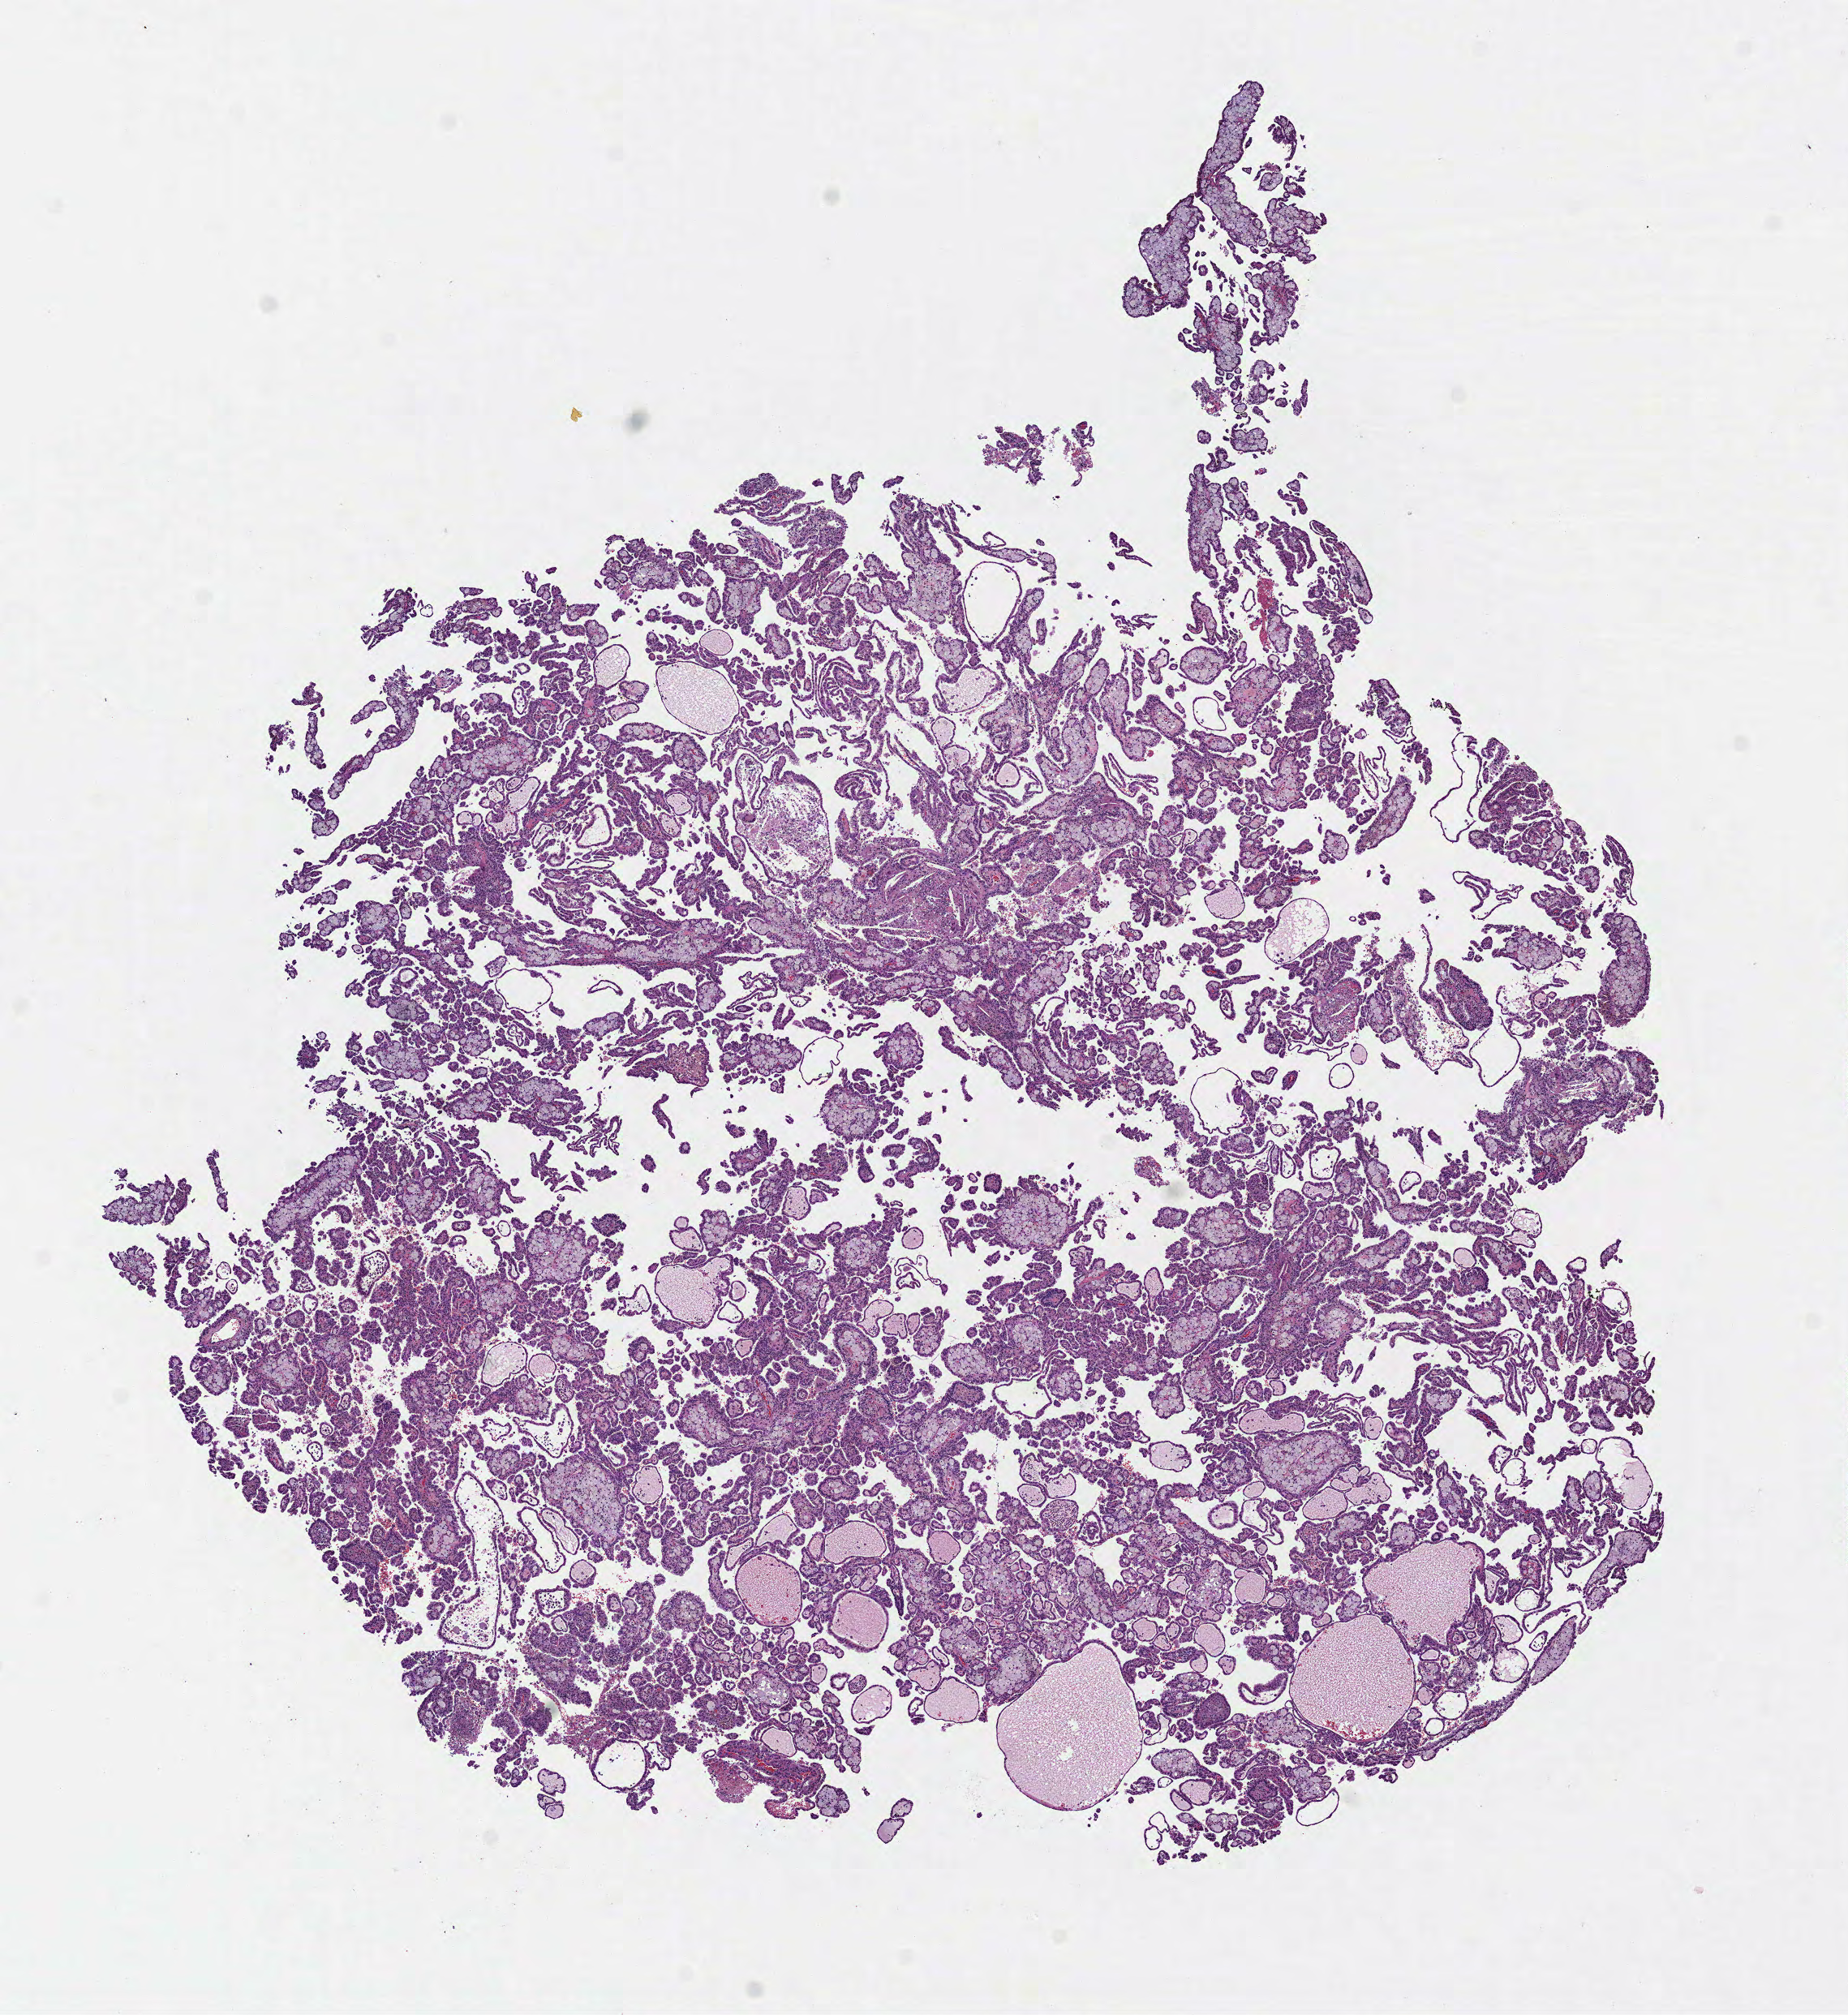
Digitized H&E tissue section (whole slide) — shown as a low-resolution overview of the whole scanned area (about 9.2 x 10.0 mm, acquisition: 40x scan); formalin-fixed paraffin-embedded (FFPE) diagnostic section; sample: primary tumour, kidney. Male patient; age at initial diagnosis 39 years.
Laterality: right. AJCC pathologic stage: I (7th edition). Diagnosis: Papillary adenocarcinoma, NOS.